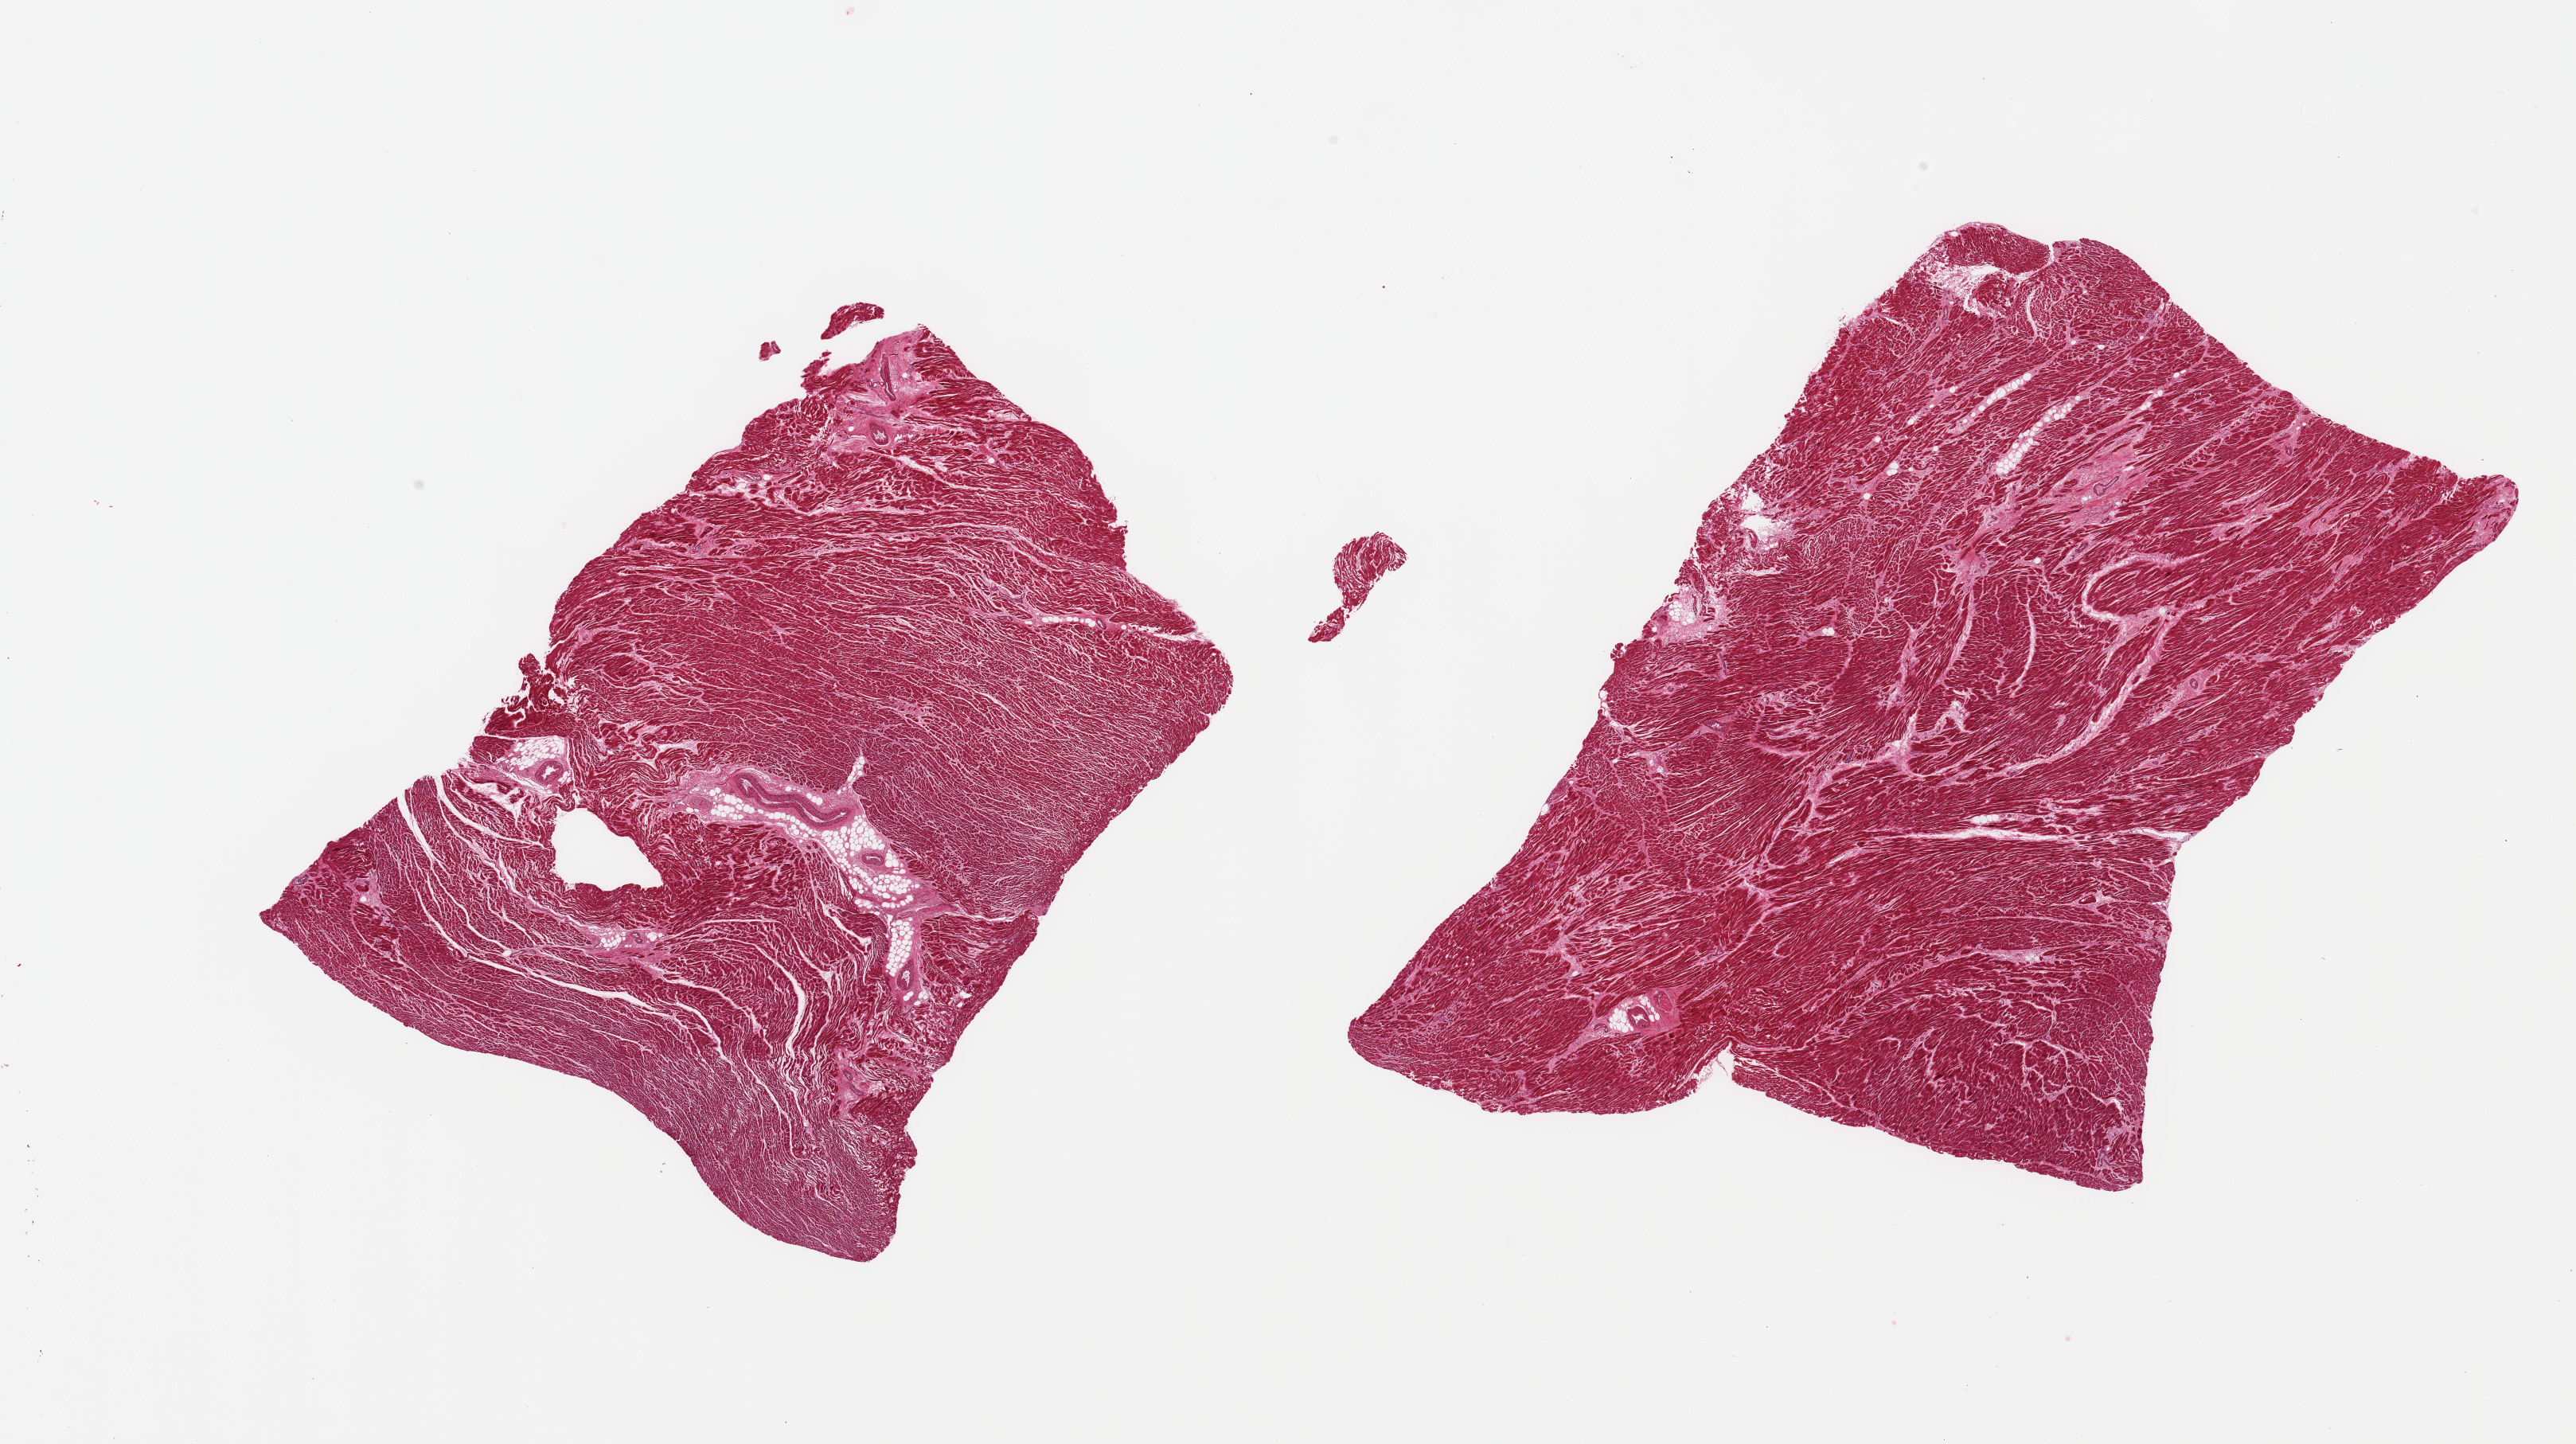
Whole-slide image, H&E stain — shown as a low-resolution overview of the whole scanned area (about 25.6 x 14.3 mm), PAXgene-fixed, paraffin-embedded tissue, sampled site (target tissue): heart, tissue donor sample. Donor sex: male.
Pathologist's review note for this sample: 2 pieces; patchy scars up to 0.8mm.